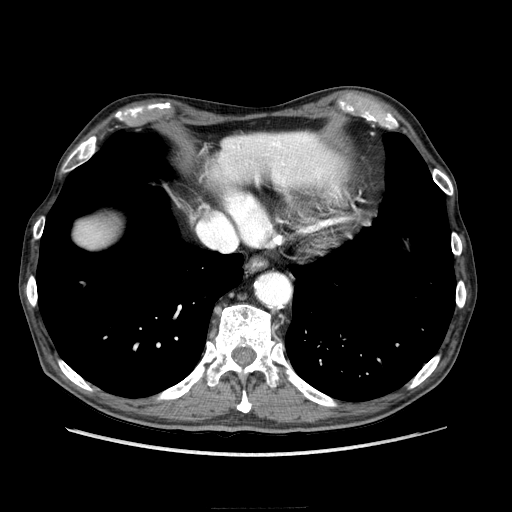
Contrast-enhanced abdominal CT (liver protocol), one axial slice; position 195 of 218 along the scan axis; reconstruction kernel STANDARD; 100 kVp; soft-tissue window (W 400 / L 40 HU); 2.5 mm slice thickness; 512 × 512 image matrix, field of view 380 × 380 mm. From the clinical record (not read from this slice): diagnosis: hepatocellular carcinoma (patient treated with transarterial chemoembolisation; whether this scan precedes or follows treatment is not stated here); TNM stage (as recorded): Stage-IIIA; Child-Pugh class: A; tumour differentiation: well differentiated; tumour nodularity: multinodular.
Annotated regions visible in this slice (semi-automatic segmentation, software-assisted and operator-edited):
- liver parenchyma outside the tumour (the mass and vessels are separate outlines, so this box may not span the whole liver): bounding box [x1, y1, x2, y2] px = [74, 221, 114, 248]